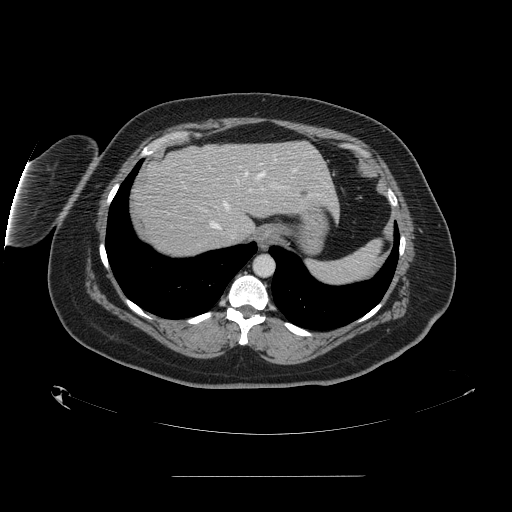
Contrast-enhanced abdominal CT, one axial slice. Slice 127 of 164 in the series (ordered by position). 120 kVp. Intravenous contrast given. Soft-tissue window (W 400 / L 40 HU). 2.5 mm slice thickness. 512 × 512 image matrix. Female patient, age 52 years. Case-level facts recorded for this patient, not image findings: diagnosis: colorectal cancer liver metastases, imaged before liver resection; multiple liver metastases: yes; largest metastasis: 3.5 cm; chemotherapy before resection: no.
Structures marked on this image (outlined manually by an expert reader):
- hepatic veins: box from (x=209, y=172) to (x=264, y=239) px
- liver: (x=133, y=142)–(x=337, y=258)
- planned liver remnant (the part of the liver to remain after resection): (x=171, y=142)–(x=337, y=228)
- portal vein (with intrahepatic branches): (x=261, y=184)–(x=272, y=190)
- liver metastasis: (x=302, y=190)–(x=308, y=197)